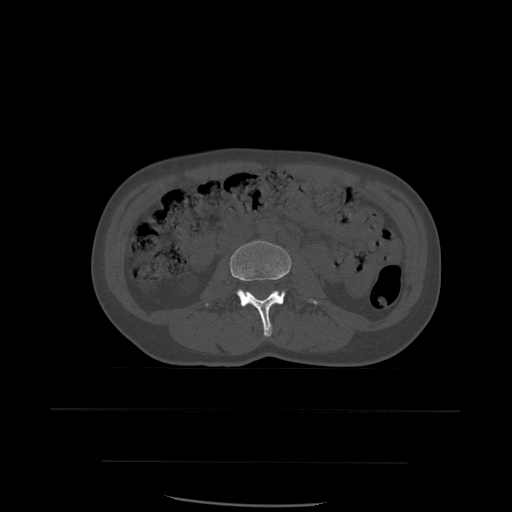
CT including the spine, one axial slice; position 196 of 574 along the scan axis; bone window (W 1800 / L 400 HU); 1.25 mm slice thickness; 512 × 512 image matrix, field of view 392 × 392 mm. Patient age 48 years. Case-level facts recorded for this patient, not image findings: primary cancer: lung.
Structures marked on this image (semi-automatically segmented with operator editing):
- L3 vertebra: bounding box (x1, y1, x2, y2) in pixels: (205, 241, 319, 337)